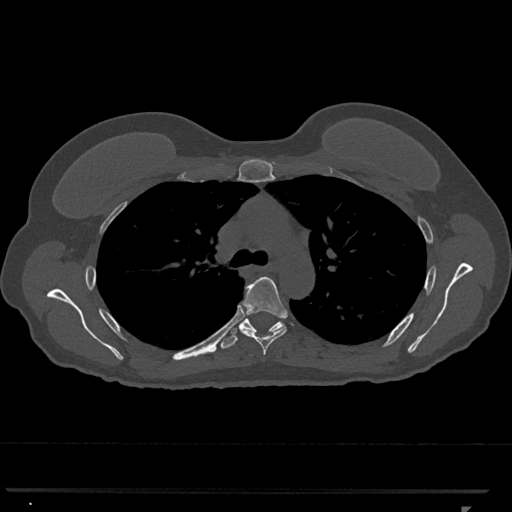
CT including the spine, one axial slice; 120 kVp; bone window (W 1800 / L 400 HU); 0.5 mm slice thickness; 512 × 512 image matrix, field of view 380 × 380 mm. Female patient, age 62 years. From the clinical record (not read from this slice): primary cancer: renal.
Outlined on this slice (semi-automatically segmented with operator editing):
- T5 vertebra: bounding box (x1, y1, x2, y2) in pixels: (240, 277, 288, 355)
- T6 vertebra: (220, 313, 283, 349)